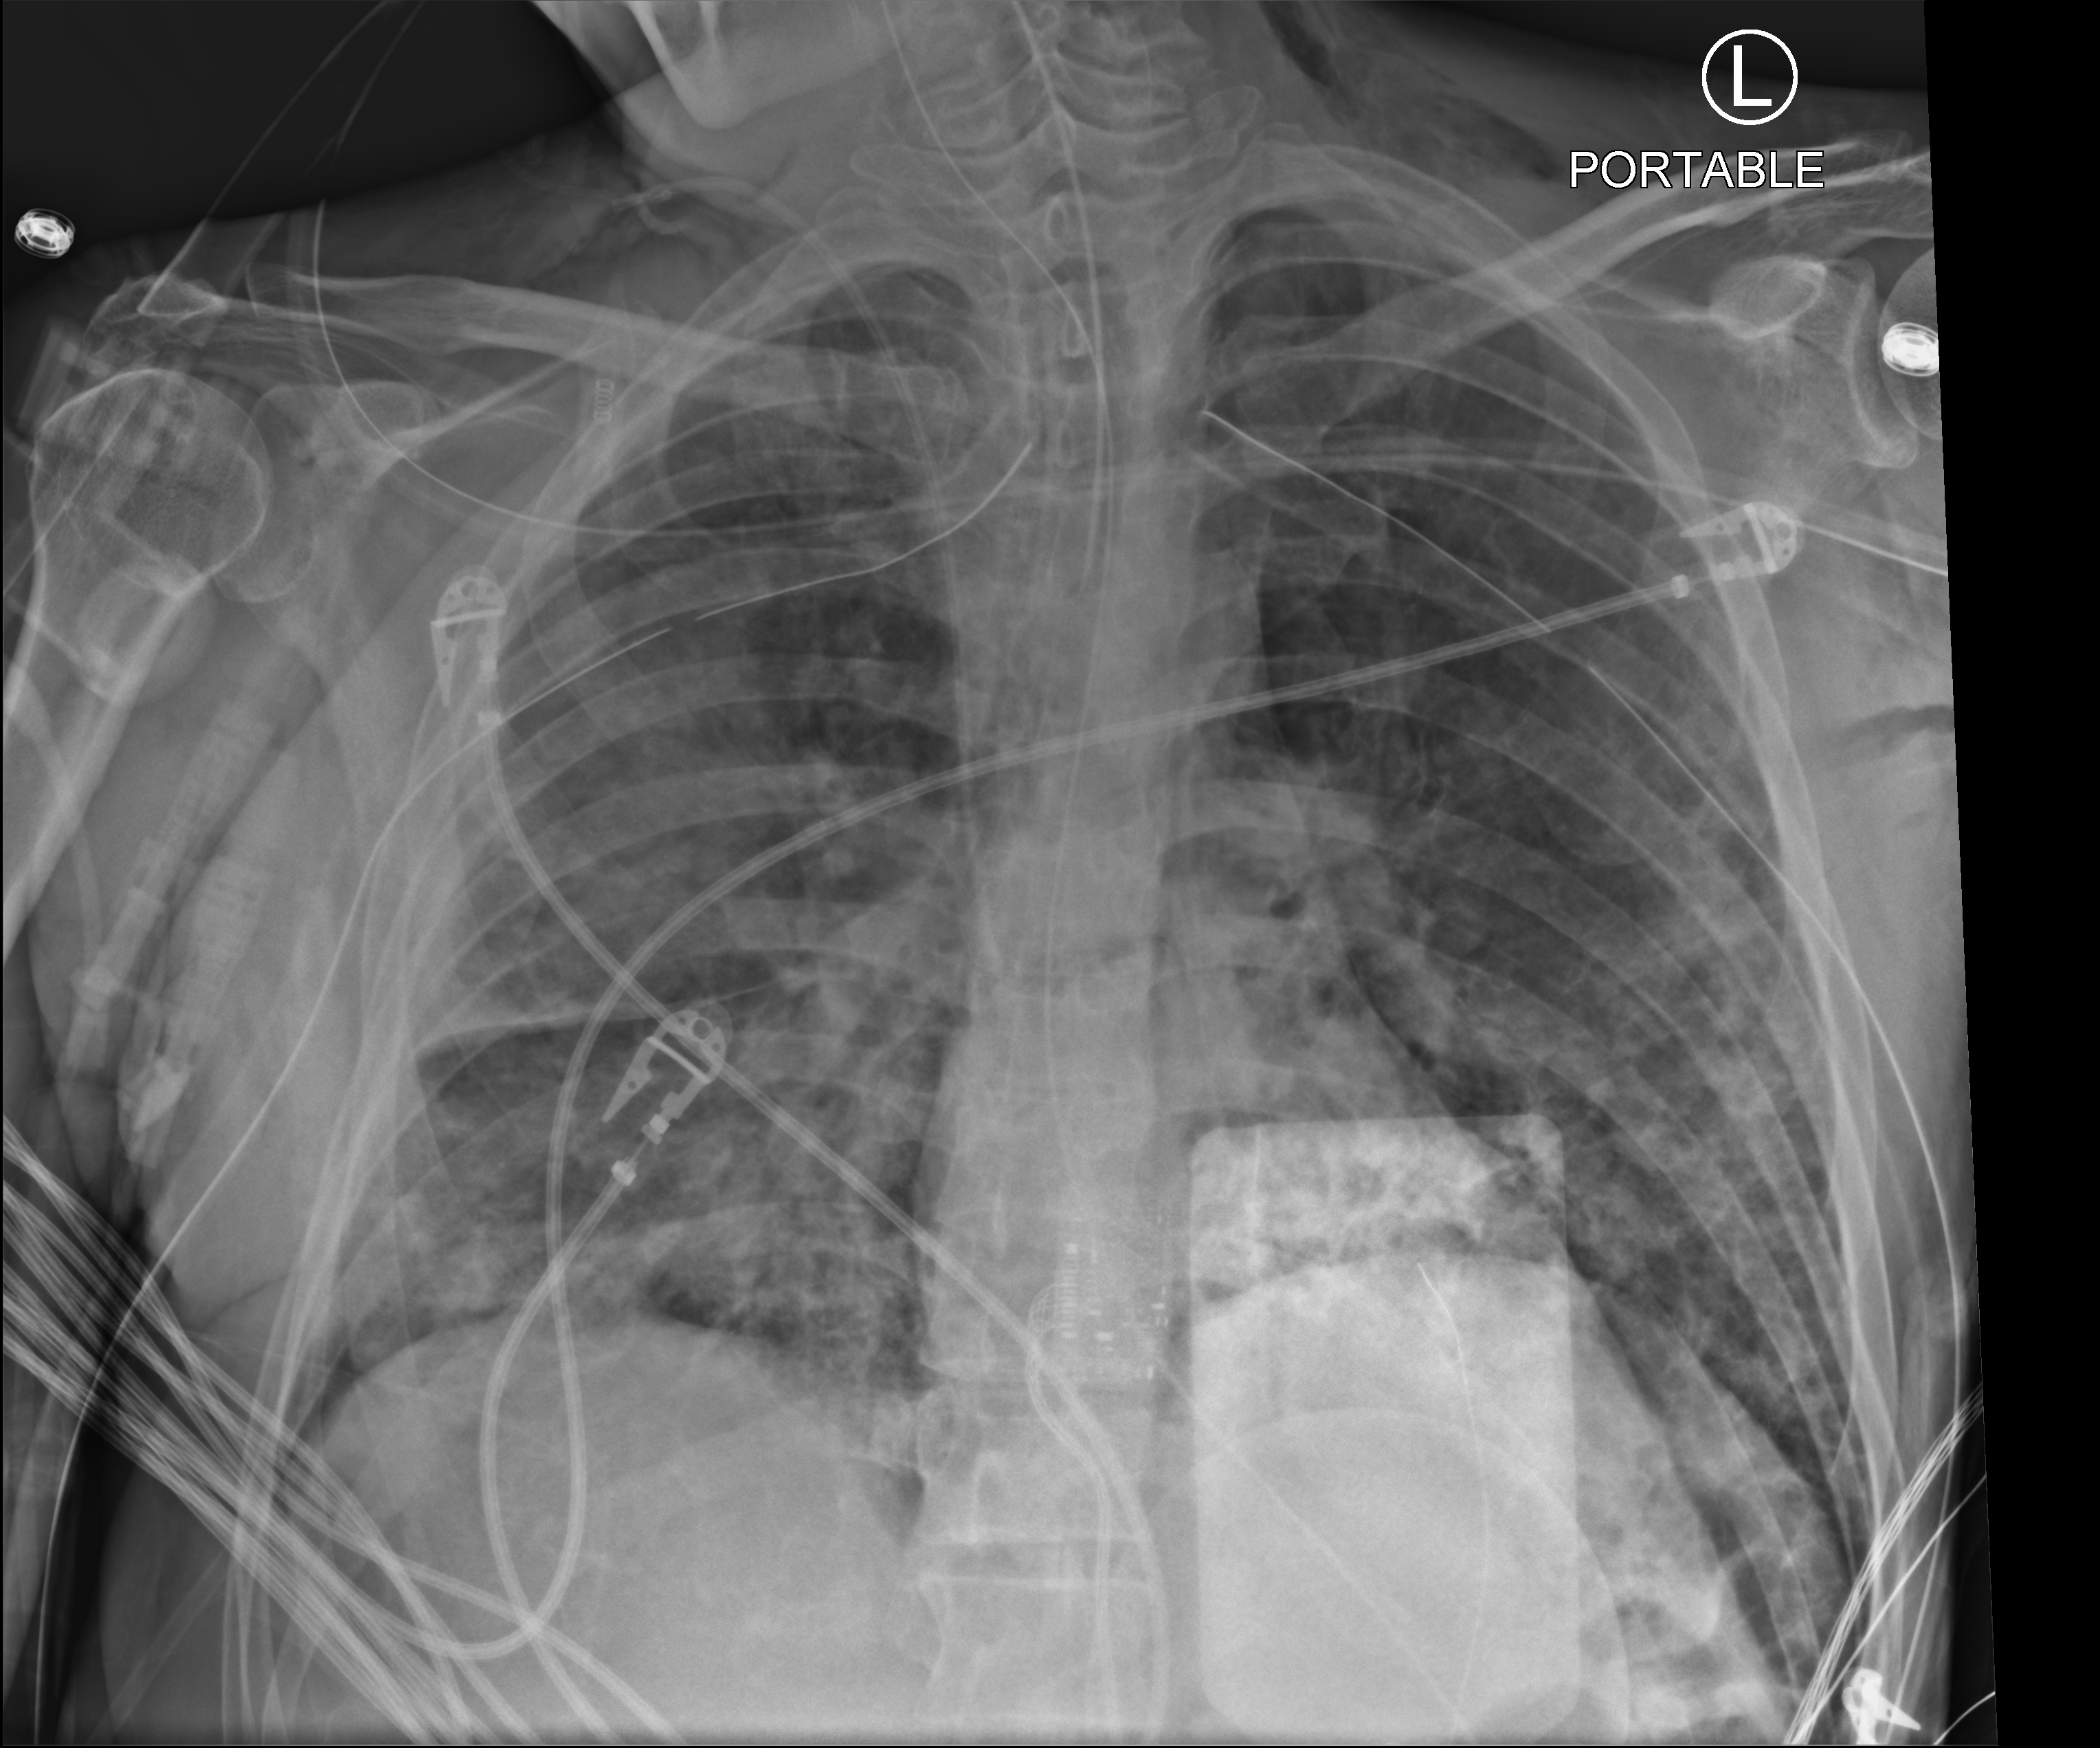
Portable chest radiograph, anteroposterior (AP) projection. Male patient hospitalised with COVID-19, age 18–59 years.
From the hospital-stay record, not from the radiograph (when in the stay this image was taken is not recorded): mechanically ventilated during this hospital stay: yes.